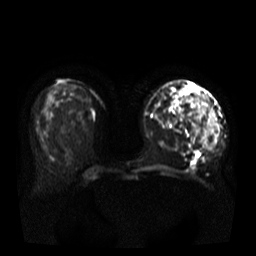
Breast MRI, one axial slice. Position 16 of 37 along the scan axis. Diffusion-weighted series; image 2 of 4 stored at this slice position (different b-values; order by instance number). 3 T. 5 mm slice thickness. 256 × 256 image matrix. Female patient.
Structures marked on this image (expert manual segmentation):
- tumour on diffusion-weighted imaging: bounding box (x1, y1, x2, y2) in pixels: (187, 96, 216, 151)